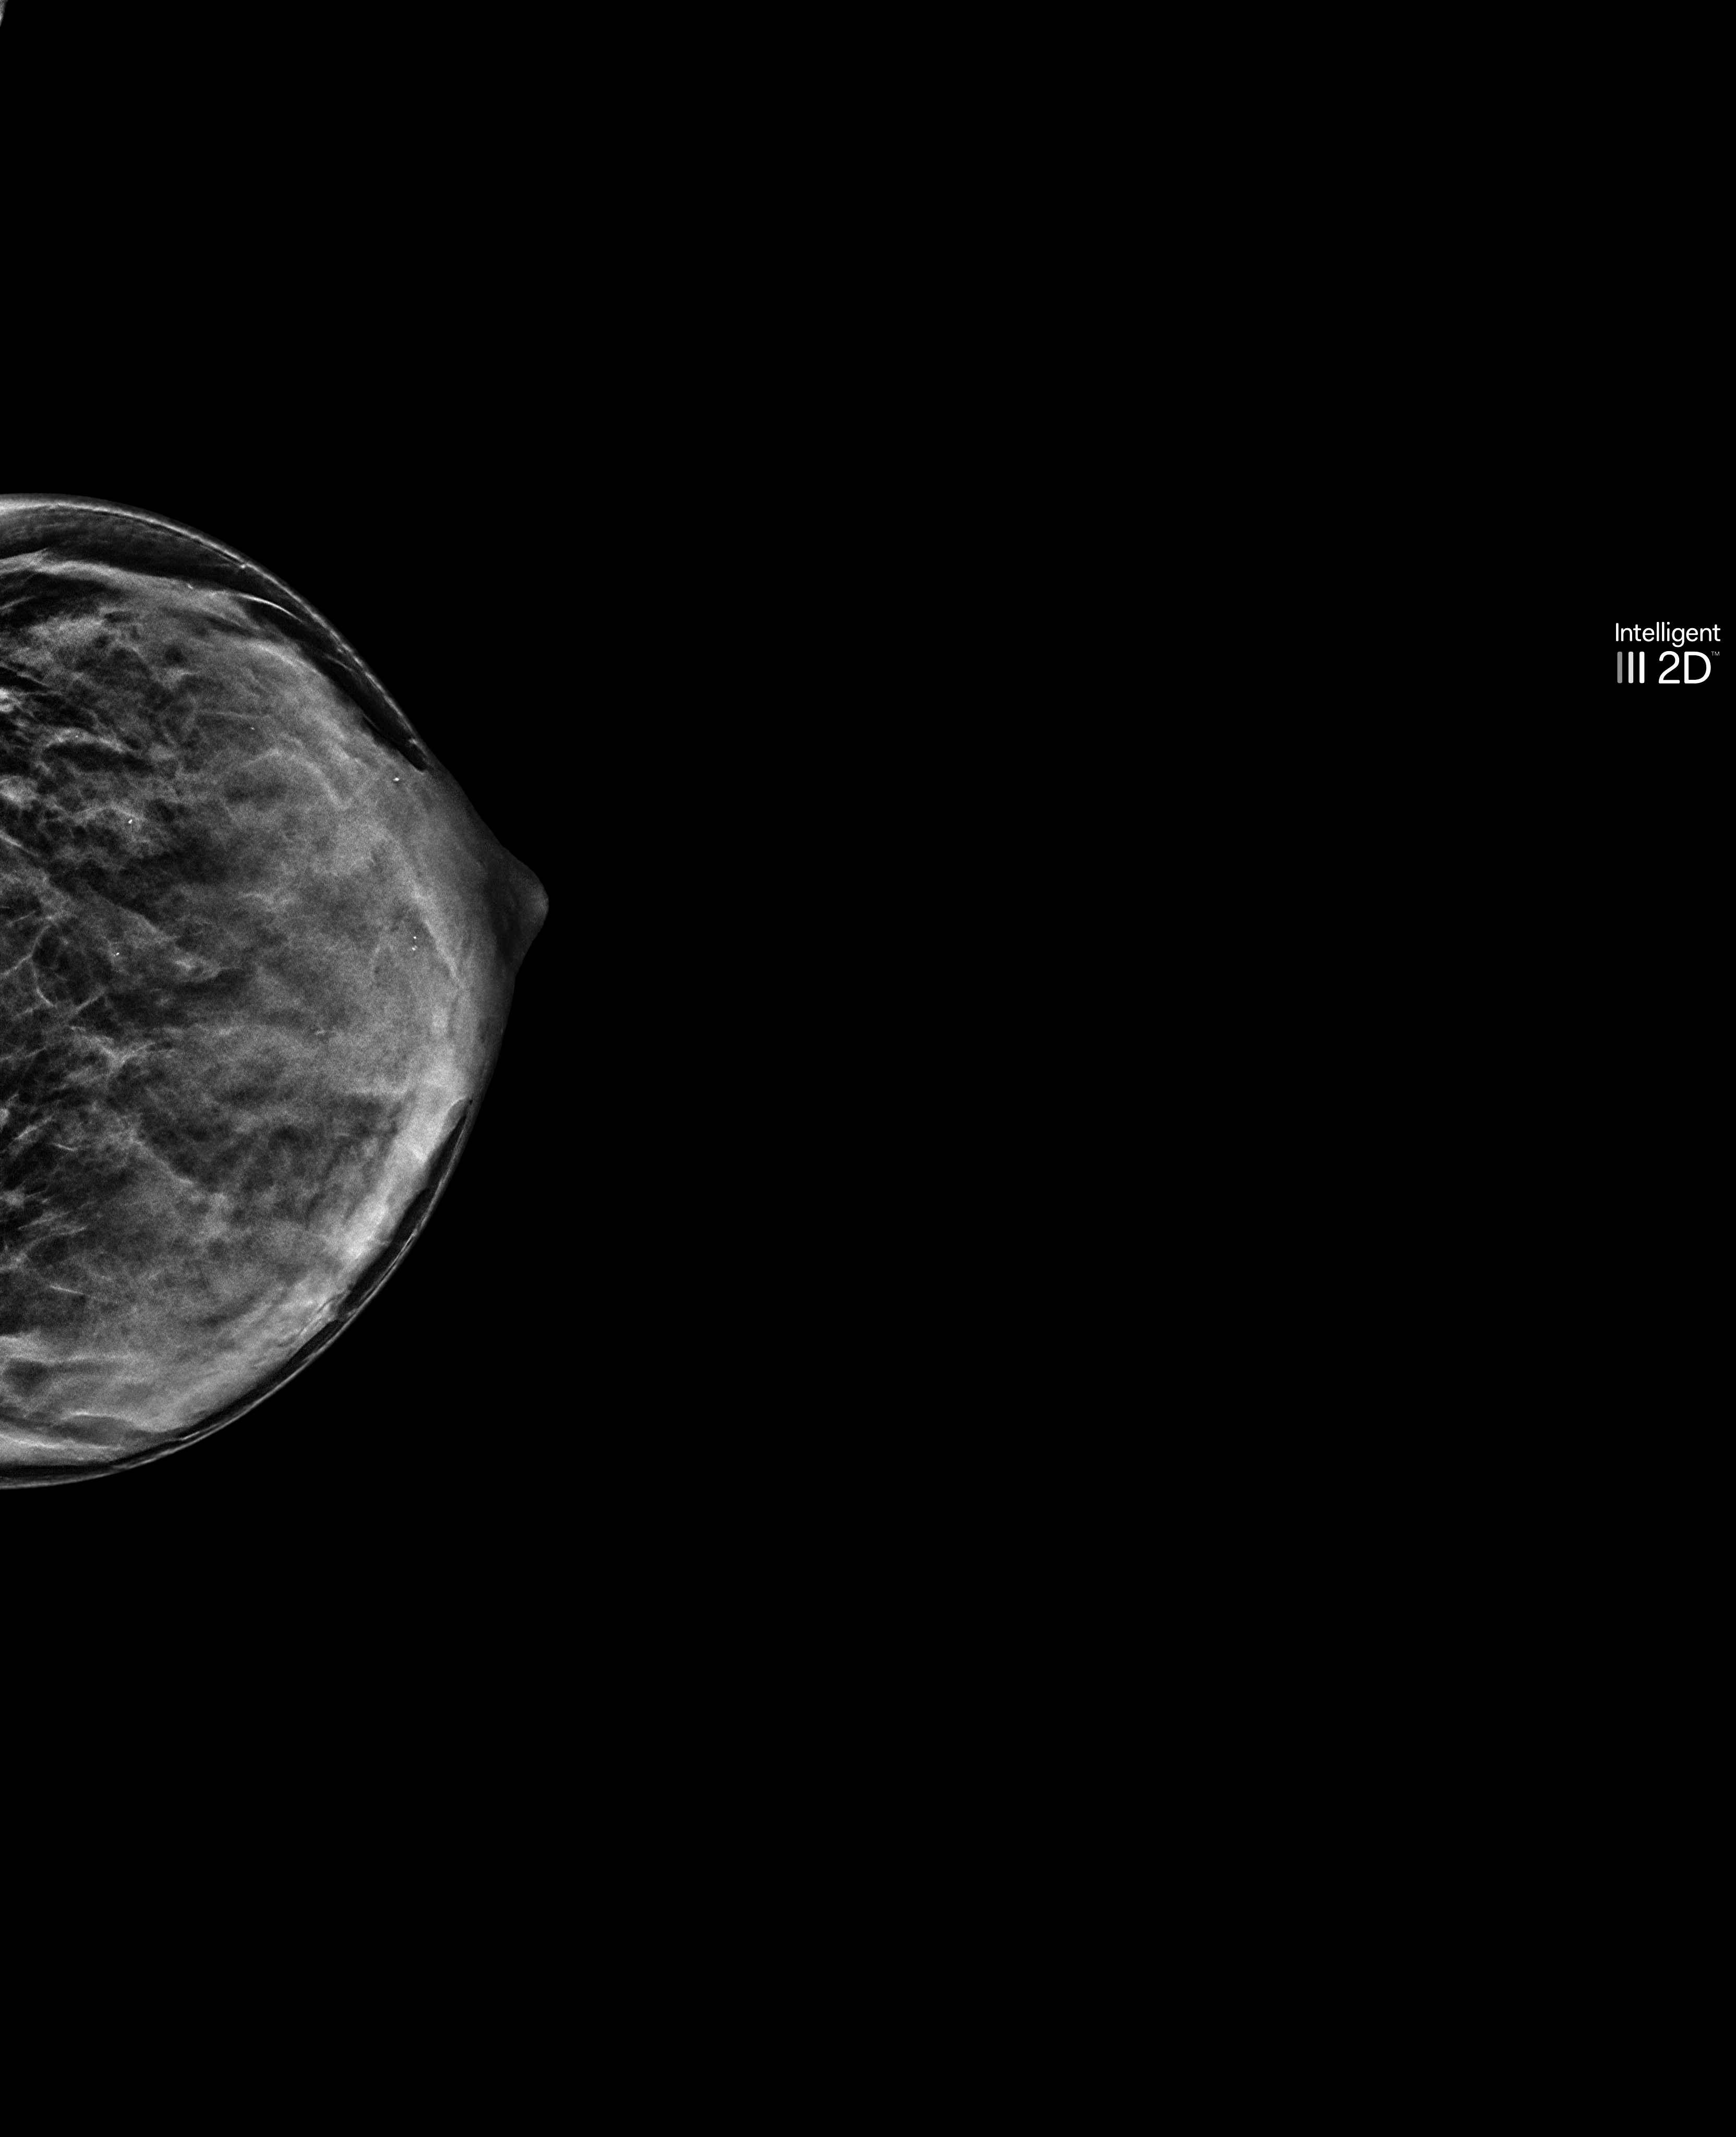
Annual screening mammography examination; system: Selenia Dimensions. Patient: female, 53 years.
Image type: synthesized 2-D view from tomosynthesis. Breast: left. Projection: craniocaudal (CC) view.